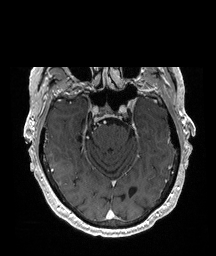
Brain MRI from a brain-tumour surgery series, one axial slice. Position 141 of 208 along the scan axis. T1-weighted post-contrast. 216 × 256 image matrix. Case-level facts recorded for this patient, not image findings: histopathology: Glioblastoma; WHO grade: 4; IDH mutation: no.
Annotated regions visible in this slice (expert manual segmentation):
- tumour: box from (x=50, y=155) to (x=70, y=175) px